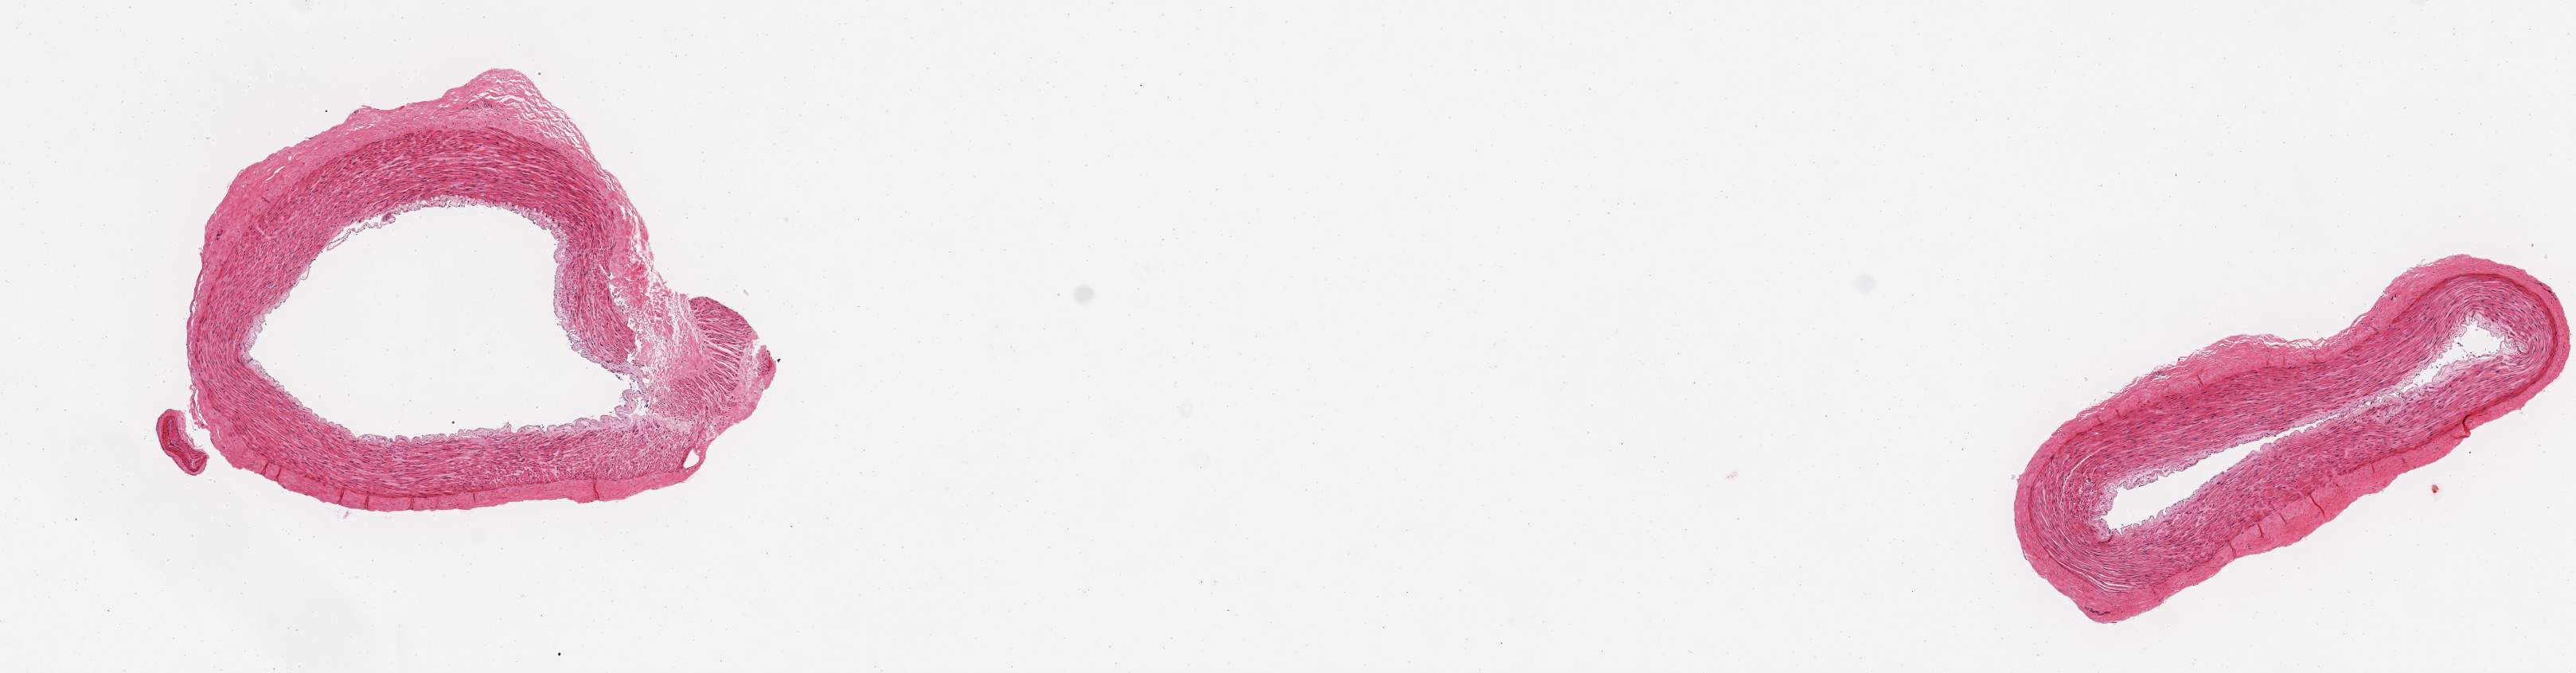
Whole-slide image, H&E stain — a low-resolution overview of the entire scanned area, about 12.8 x 3.3 mm (from a 20x scan). PAXgene-fixed paraffin-embedded (PFPE) section. Section of tibial artery (target tissue). Donor tissue sample. Male donor.
Reviewer comment on this tissue sample: 2 pieces; no plaques; well dissected.